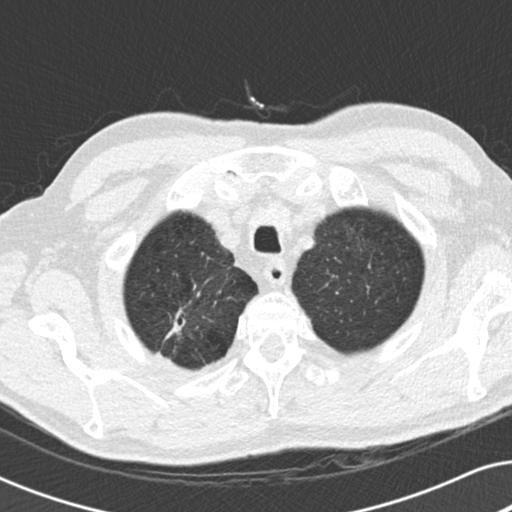
Low-dose screening chest CT, one axial slice. Position 169 of 191 along the scan axis. Lung window (W 1500 / L -600 HU). 2 mm slice thickness. 512 × 512 image matrix, field of view 330 × 330 mm.
Structures marked on this image (manually delineated by an expert):
- lesion 2 (nodule, lower lobe of right lung): bounding box (x1, y1, x2, y2) in pixels: (166, 309, 186, 338)